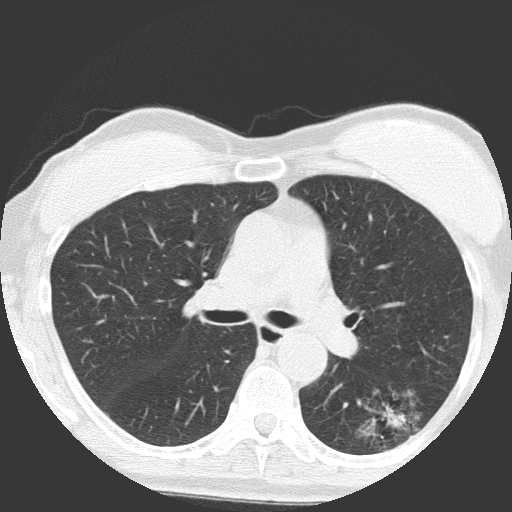
Chest CT (low-dose screening protocol), one axial image, first (baseline) screen, lung window (W 1500 / L -600 HU), lung (sharp) reconstruction kernel (FC51), slice 57 of 149 in the series. Female participant, aged 64 years at enrolment. Former smoker at enrolment.
Lesion marked by an expert reader, bounding box (x1, y1, x2, y2) in pixels: (343, 387, 429, 459). Reader record for this screening exam (exam-level; its link to the box is not recorded): non-calcified nodule or mass ≥4 mm, right upper lobe, 4 × 4 mm, poorly defined margins, ground glass attenuation. Note: the box lies in the patient's left hemithorax on this image, whereas the reader's record names the right lung; they may be different findings. Participant outcome: lung cancer diagnosed 932 days after this screen (after the third annual screen) — adenocarcinoma, NOS, left lower lobe, moderately differentiated (G2), stage IA (AJCC 6th edition), 17 mm at pathology.